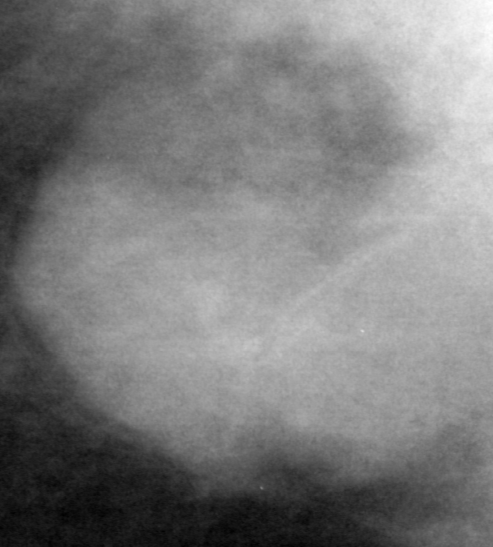
Crop from a digitized film mammogram around one marked abnormality; right breast; CC view.
Mass, shape lobulated, margins obscured; BI-RADS assessment category 4; subtlety rating 3 on a 1 (subtle) to 5 (obvious) scale; pathology result (as recorded, not read from the image): benign.